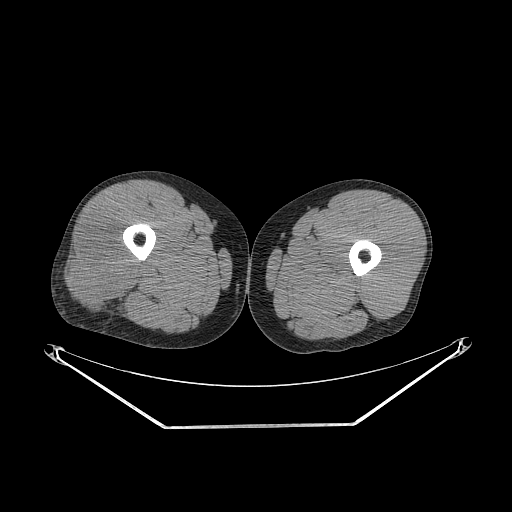
CT of an extremity soft-tissue mass (from a PET/CT study), one axial slice. Position 244 of 267 along the scan axis. Reconstruction kernel STANDARD. 140 kVp. Soft-tissue window (W 400 / L 40 HU). 512 × 512 image matrix, field of view 500 × 500 mm. Male patient. From the clinical record (not read from this slice): histological type: poorly differentiated synovial sarcoma; grade: high; site of the primary tumour: right buttock.
Structures marked on this image (expert contour drawn on MRI and transferred to this co-registered scan by the dataset authors):
- gross tumour volume including surrounding oedema: bounding box (x1, y1, x2, y2) in pixels: (71, 222, 138, 307)
- gross tumour volume (mass): (73, 222, 138, 307)